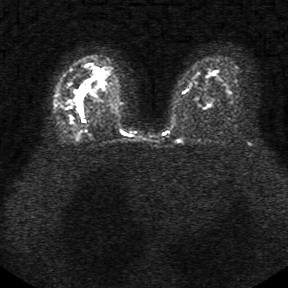
Breast MRI, one axial slice; position 20 of 34 along the scan axis; diffusion-weighted series; image 2 of 4 stored at this slice position (different b-values; order by instance number); 1.5 T; 5 mm slice thickness; 288 × 288 image matrix. Female patient.
Structures marked on this image (manually delineated by an expert):
- tumour on diffusion-weighted imaging: box from (x=75, y=80) to (x=91, y=117) px